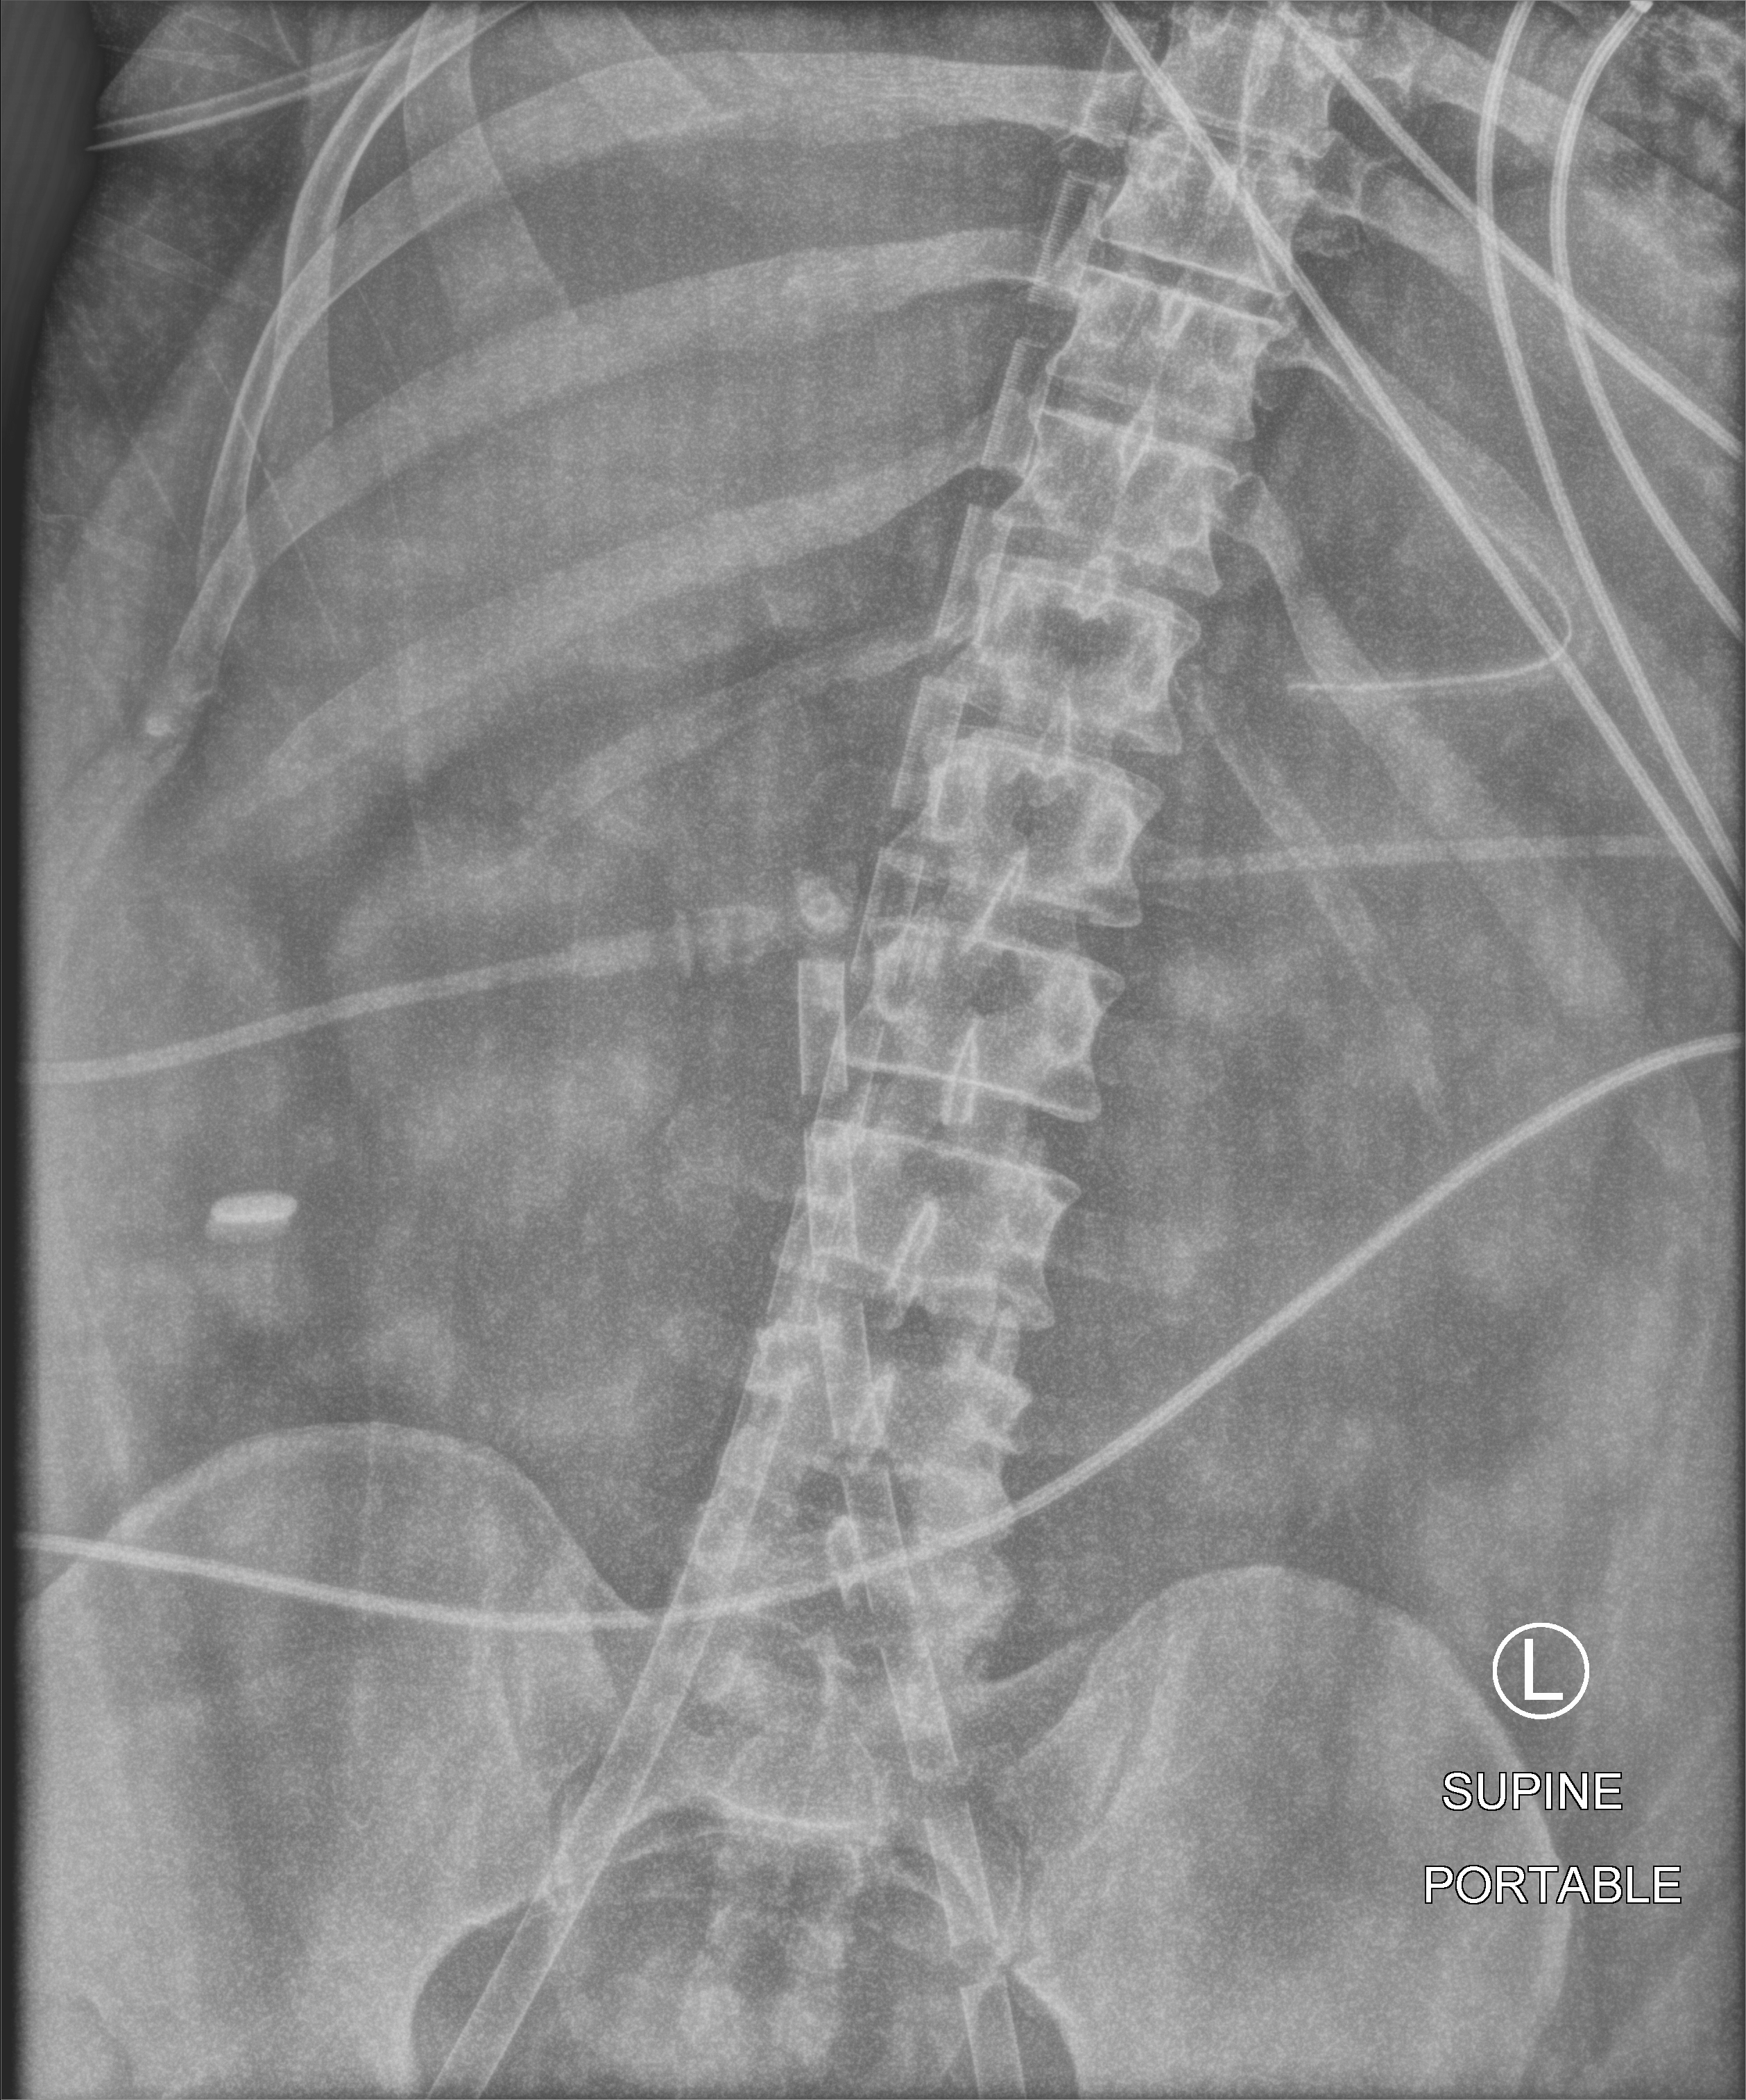
Abdomen X-ray (portable); anteroposterior (AP) projection. Adult patient hospitalised with COVID-19, age 18–59 years.
Admission-level facts for this patient (not findings on this image; timing relative to this image not recorded):
- mechanically ventilated during this hospital stay: yes